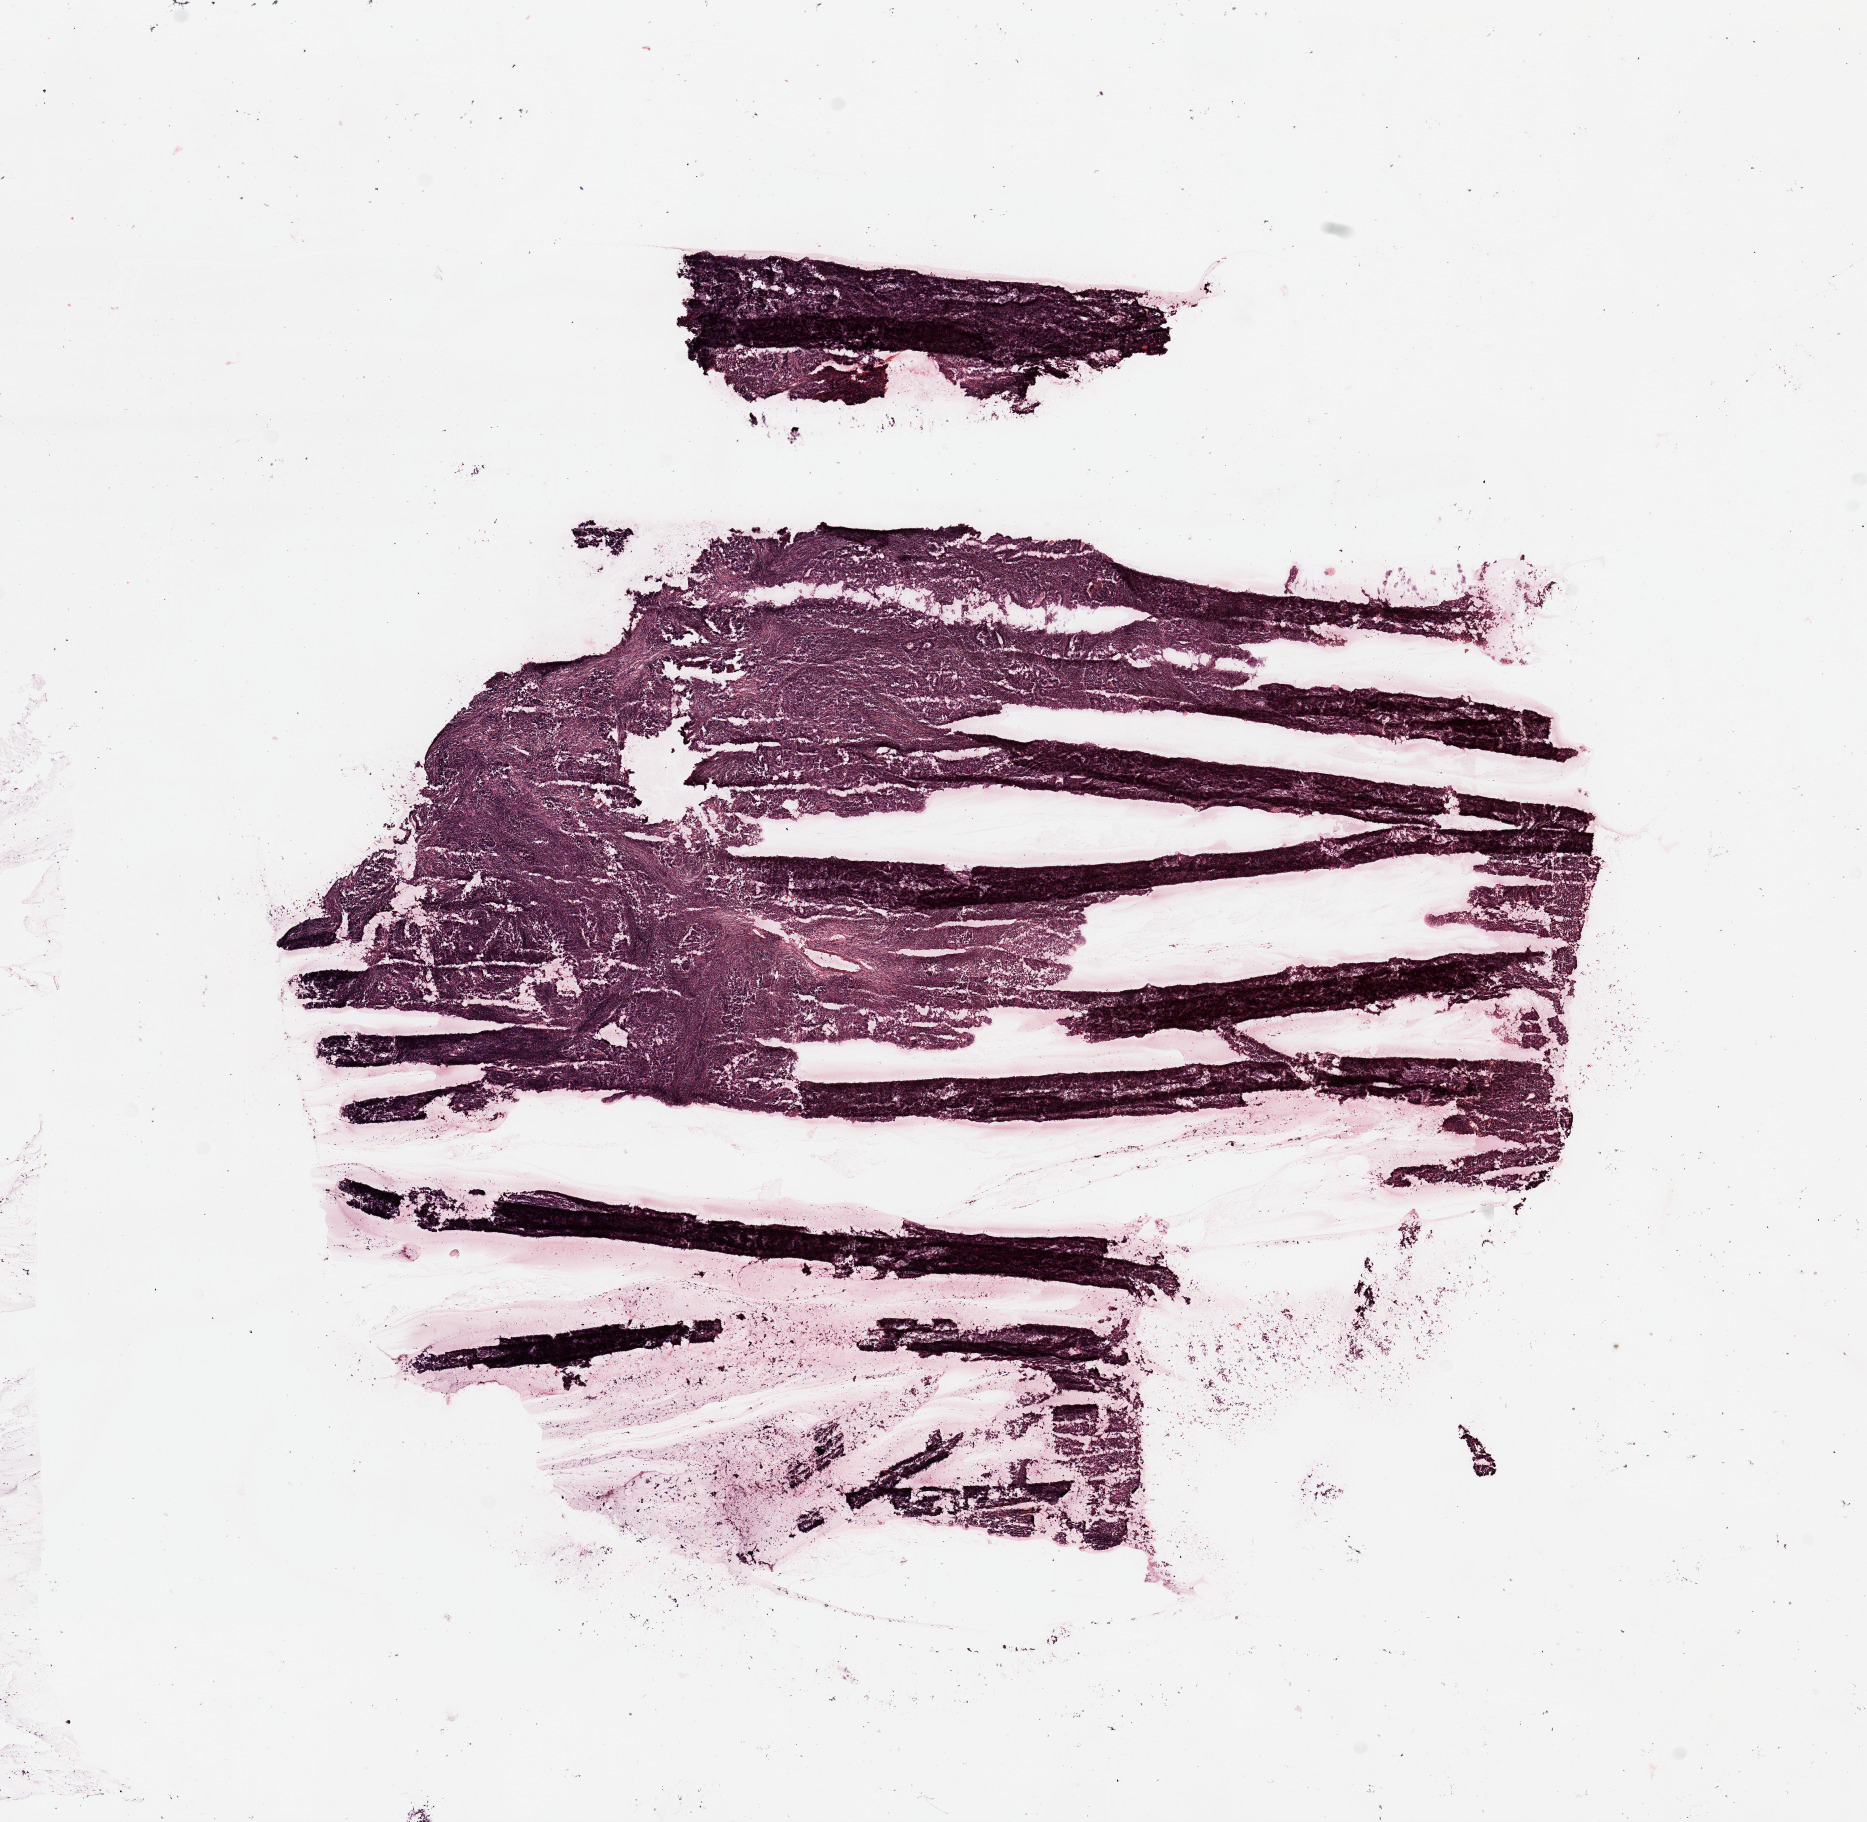
Whole-slide histology image, H&E, low-resolution overview of the scanned area, about 14.8 x 14.4 mm (slide scanned at 20x); tumour tissue sample, uterus. Female, 62 y/o.
Diagnosis: Endometrioid adenocarcinoma, NOS.